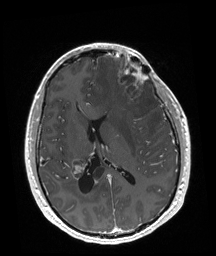
Brain MRI from a brain-tumour surgery series, one axial slice; slice 84 of 192 in the series (ordered by position); T1-weighted post-contrast; 1 mm slice thickness; 216 × 256 image matrix, field of view 219 × 260 mm.
Outlined on this slice (outlined manually by an expert reader):
- tumour: box from (x=117, y=58) to (x=147, y=103) px